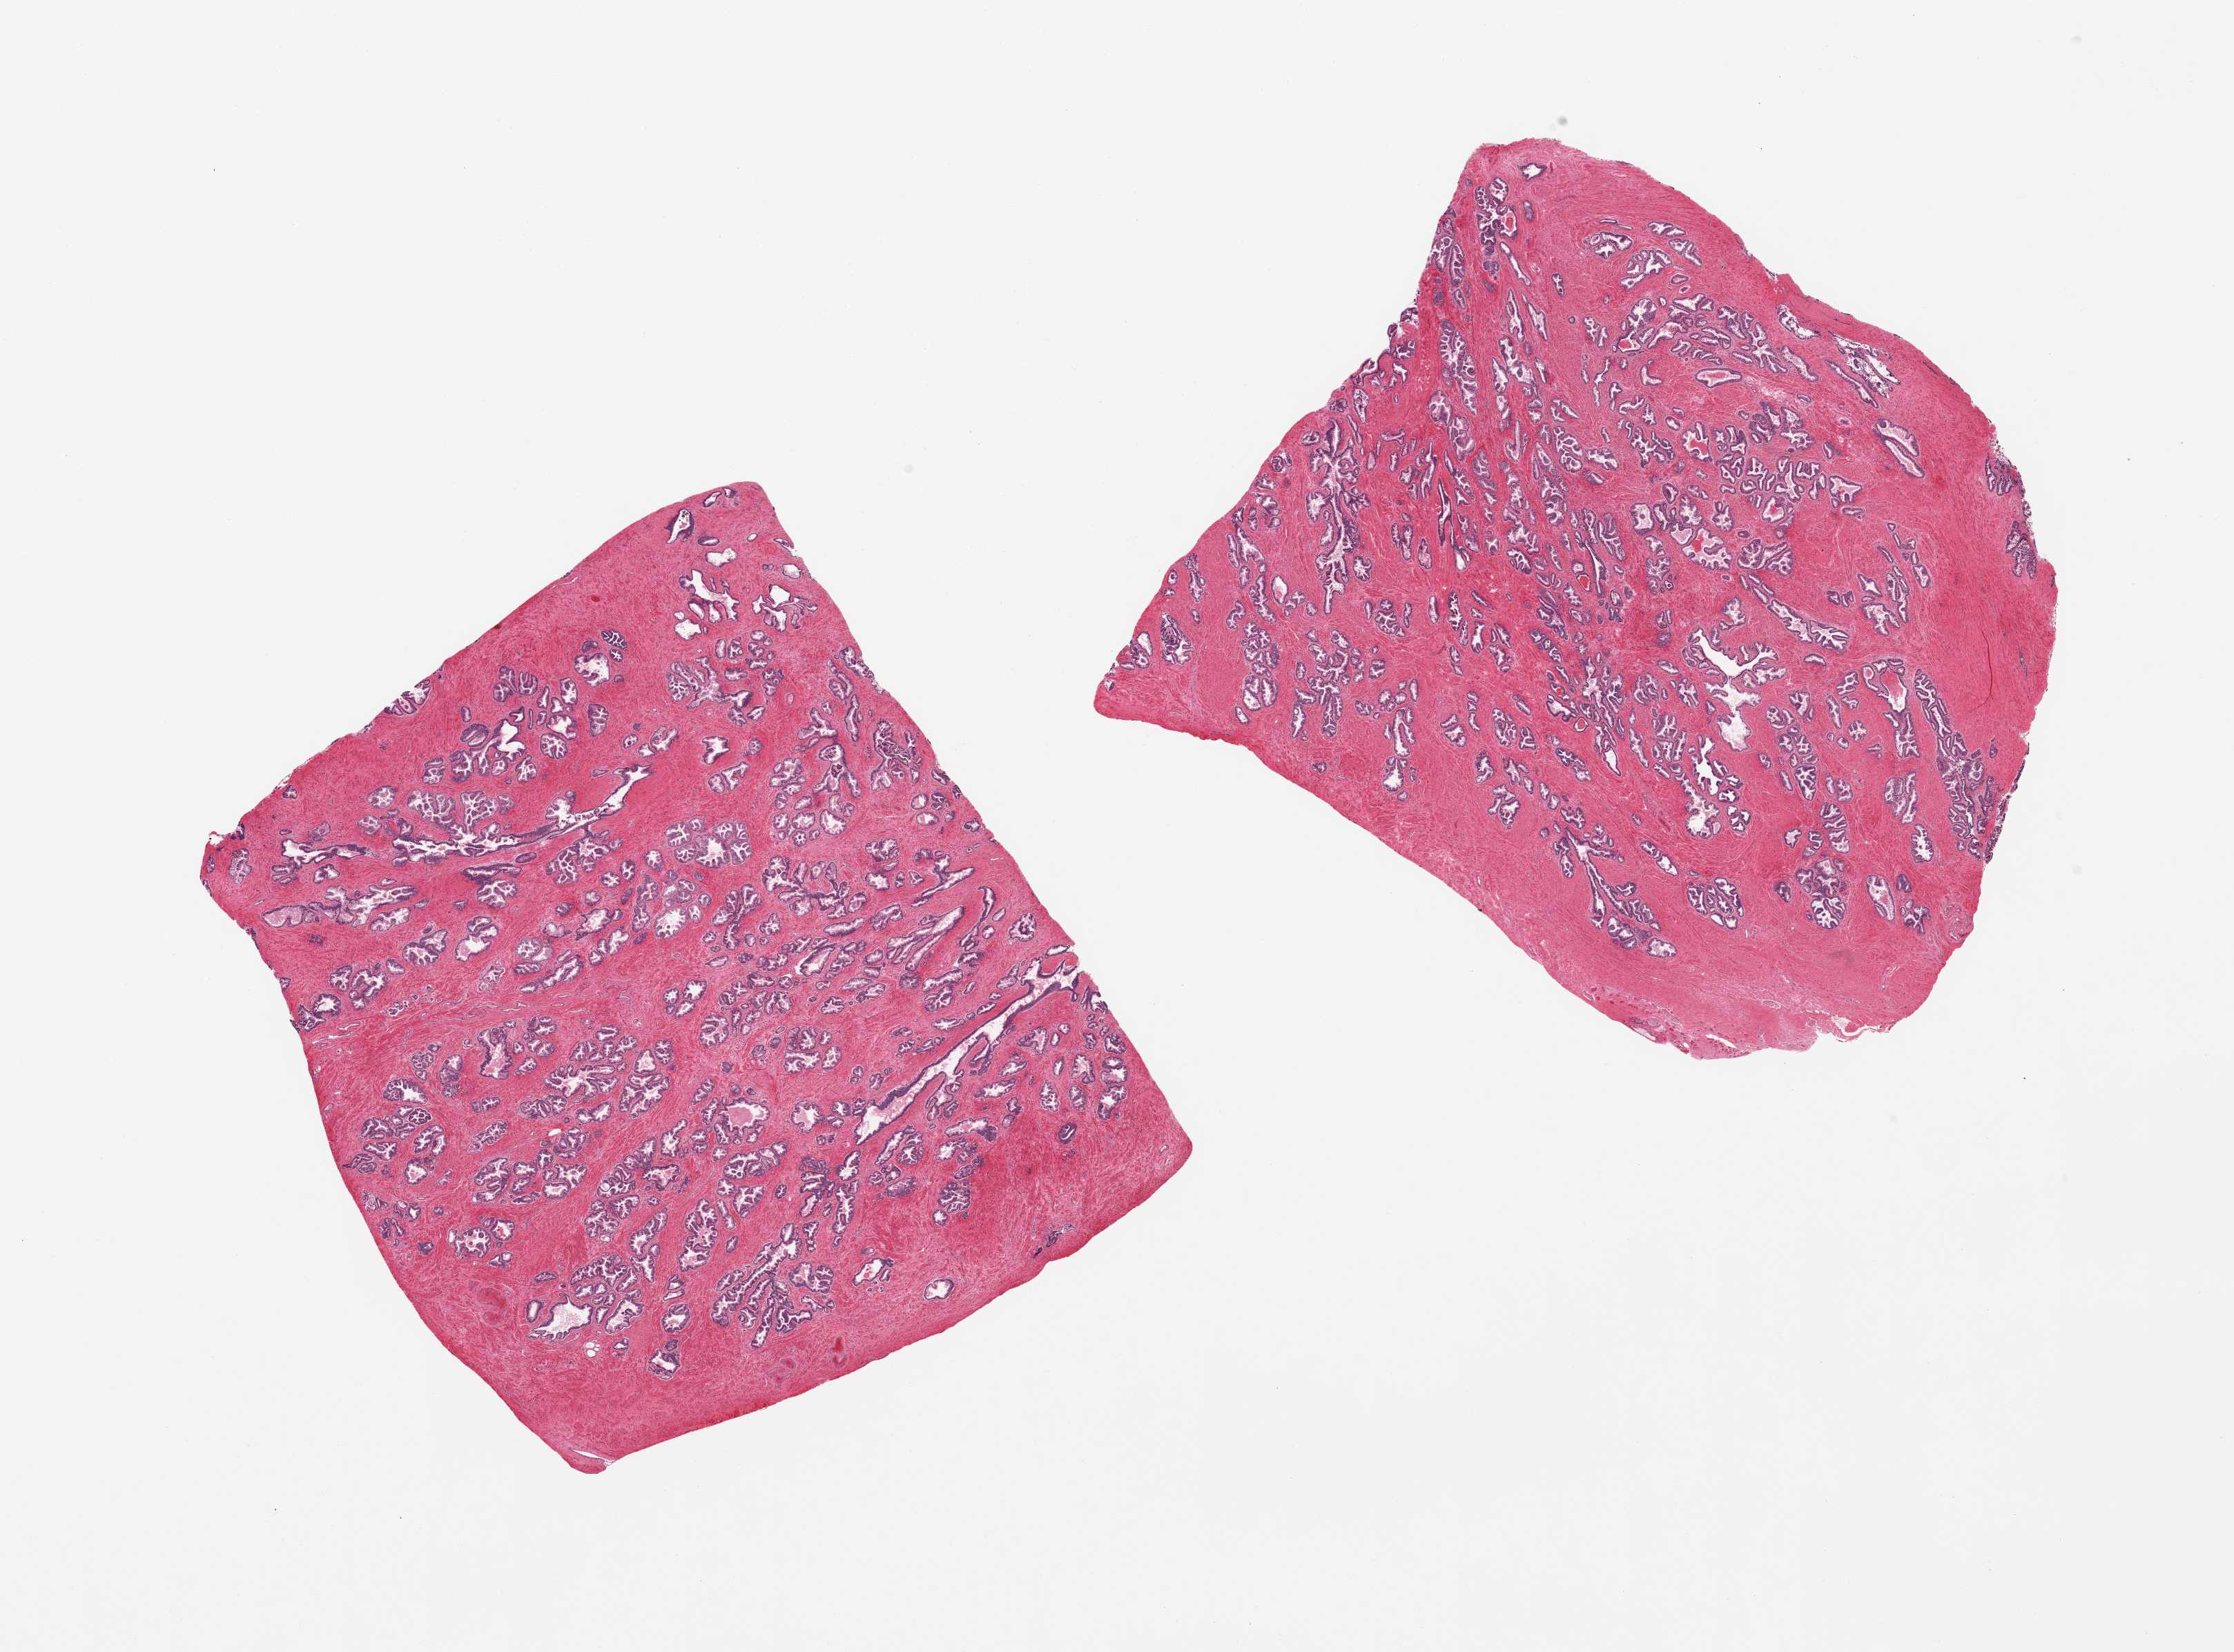
H&E whole-slide image, brightfield, whole scanned area (about 25.6 x 18.9 mm) shown as a low-resolution overview; PAXgene-fixed paraffin-embedded (PFPE) section; section of prostate (target tissue); donor tissue sample. Donor sex: male.
* pathologist's review note for this sample: 2 pieces; good distribution of stroma and glands with small focus of skeletal muscle and nerve at periphery of one piece